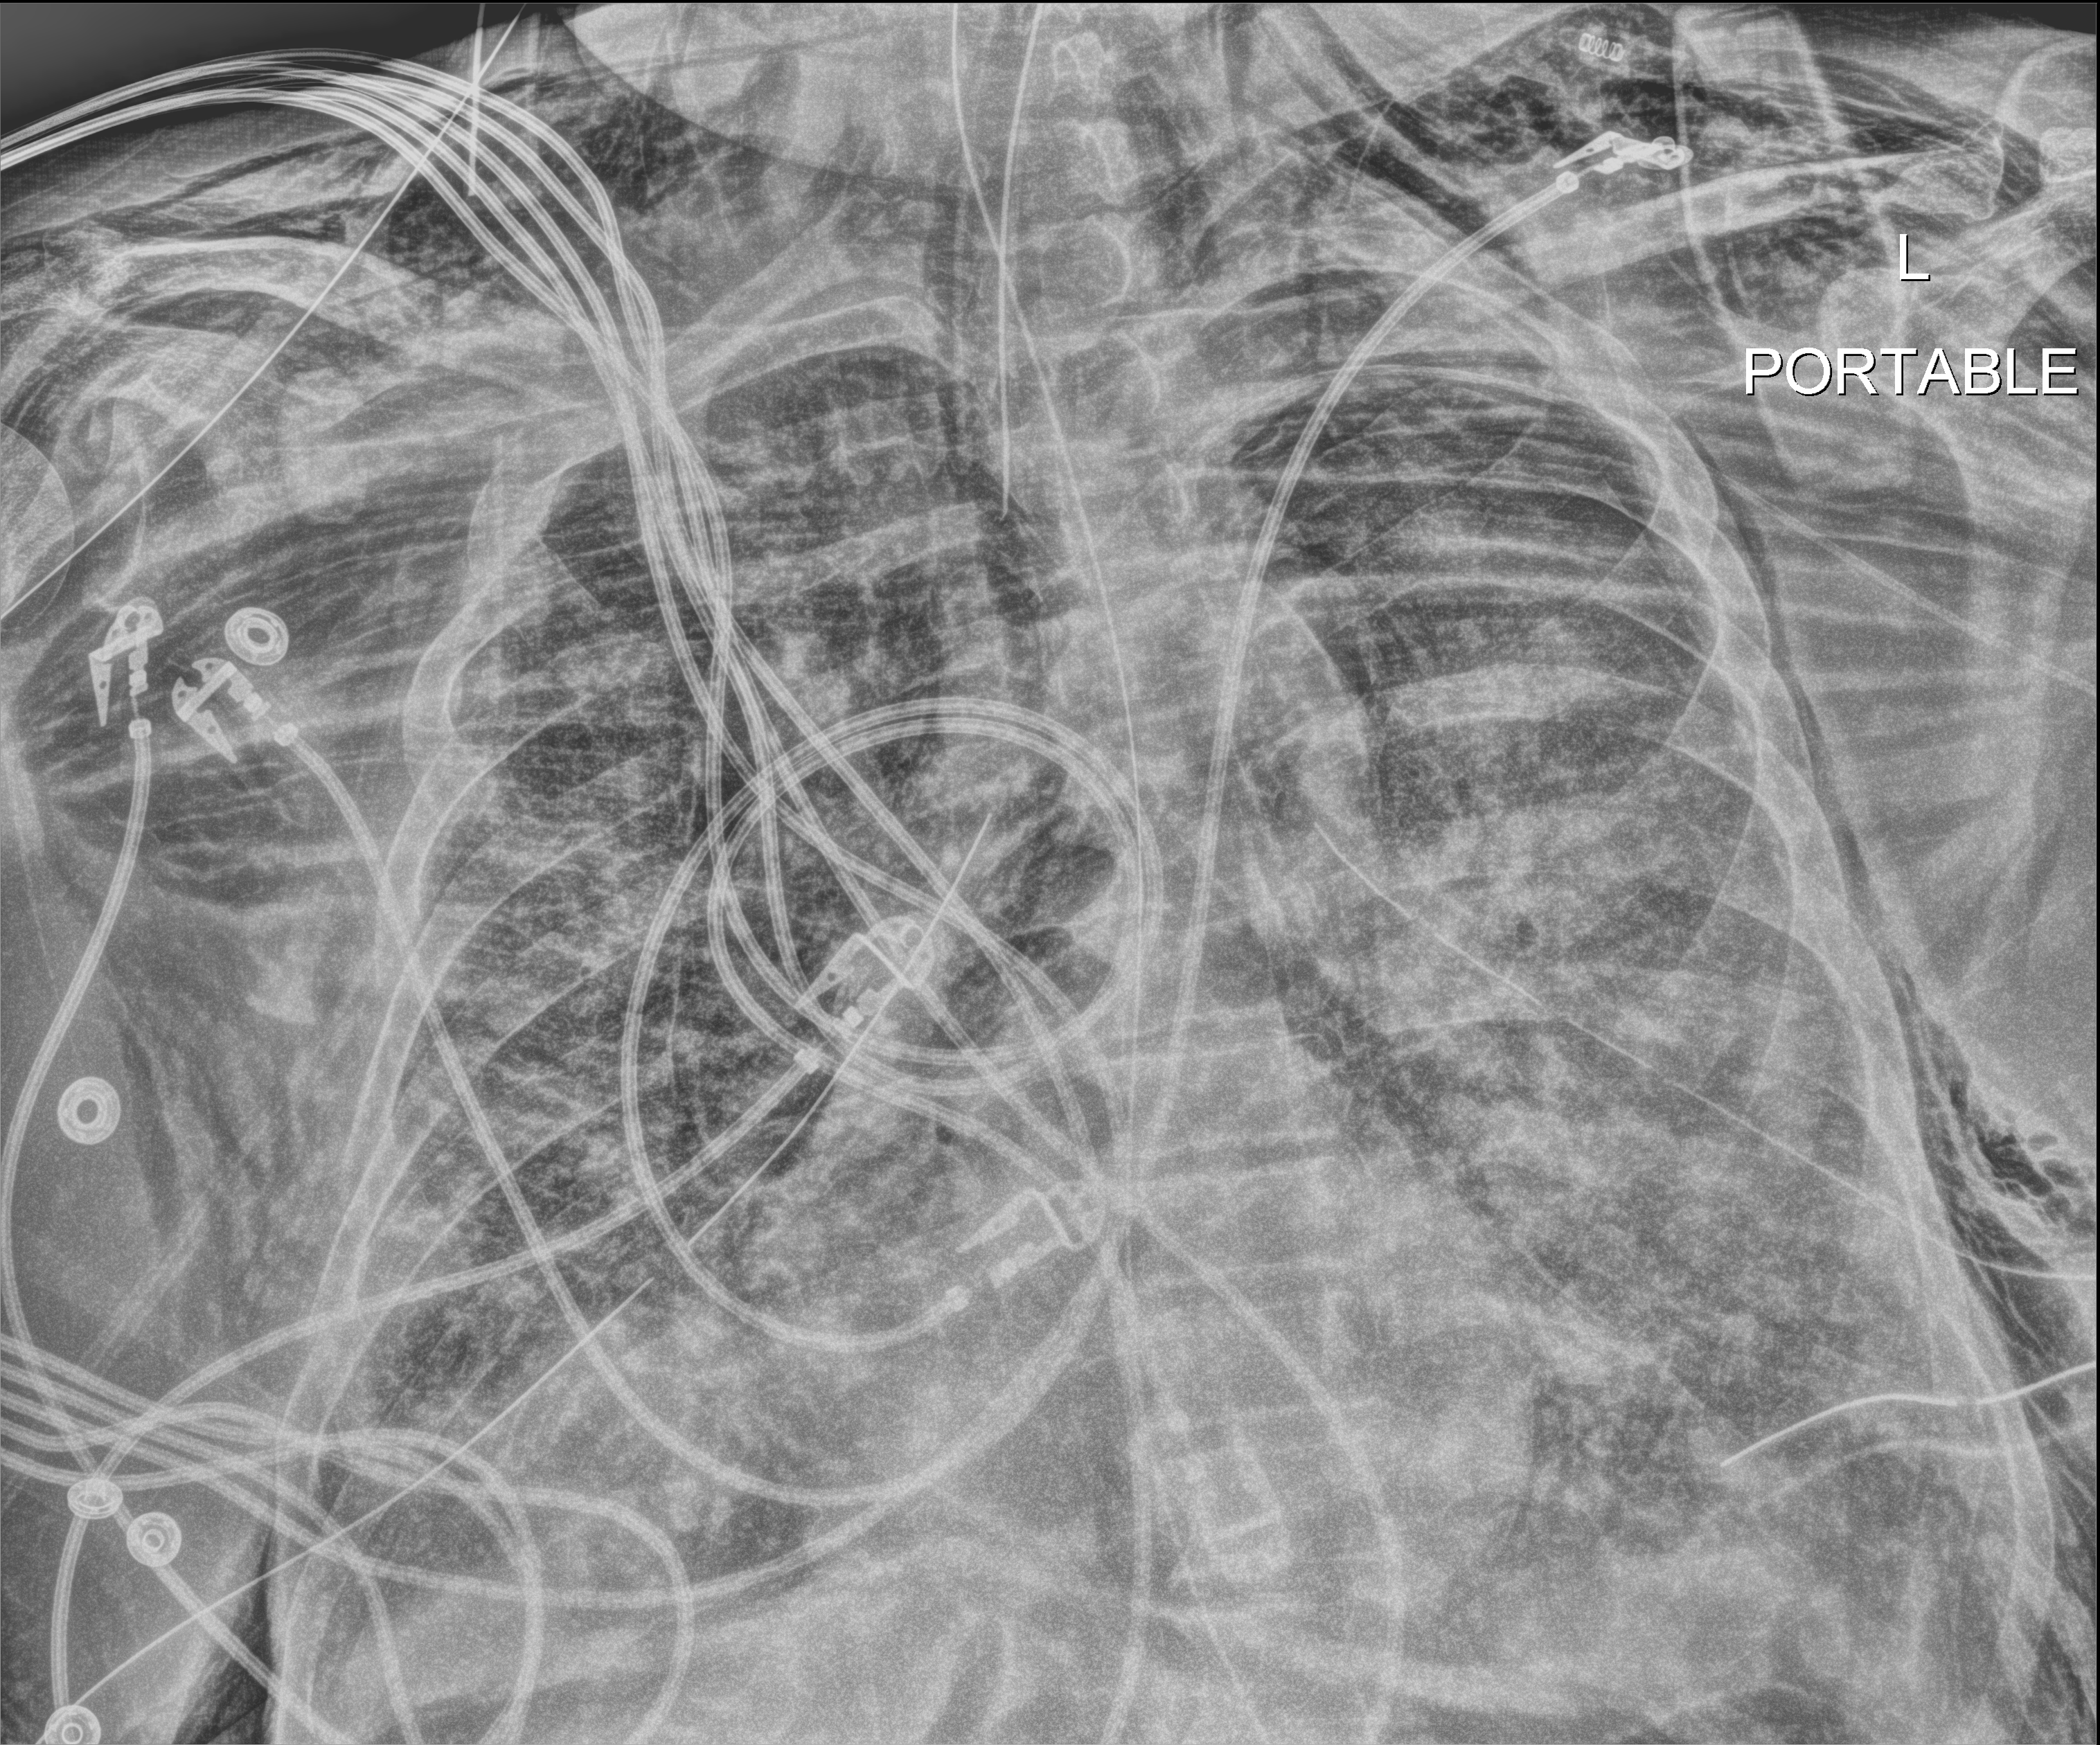
Portable chest radiograph; anteroposterior (AP) projection. Adult patient hospitalised with COVID-19, age 18–59 years.
Admission-level facts for this patient (not findings on this image; timing relative to this image not recorded):
- admitted to intensive care during this hospital stay: yes
- mechanically ventilated during this hospital stay: yes